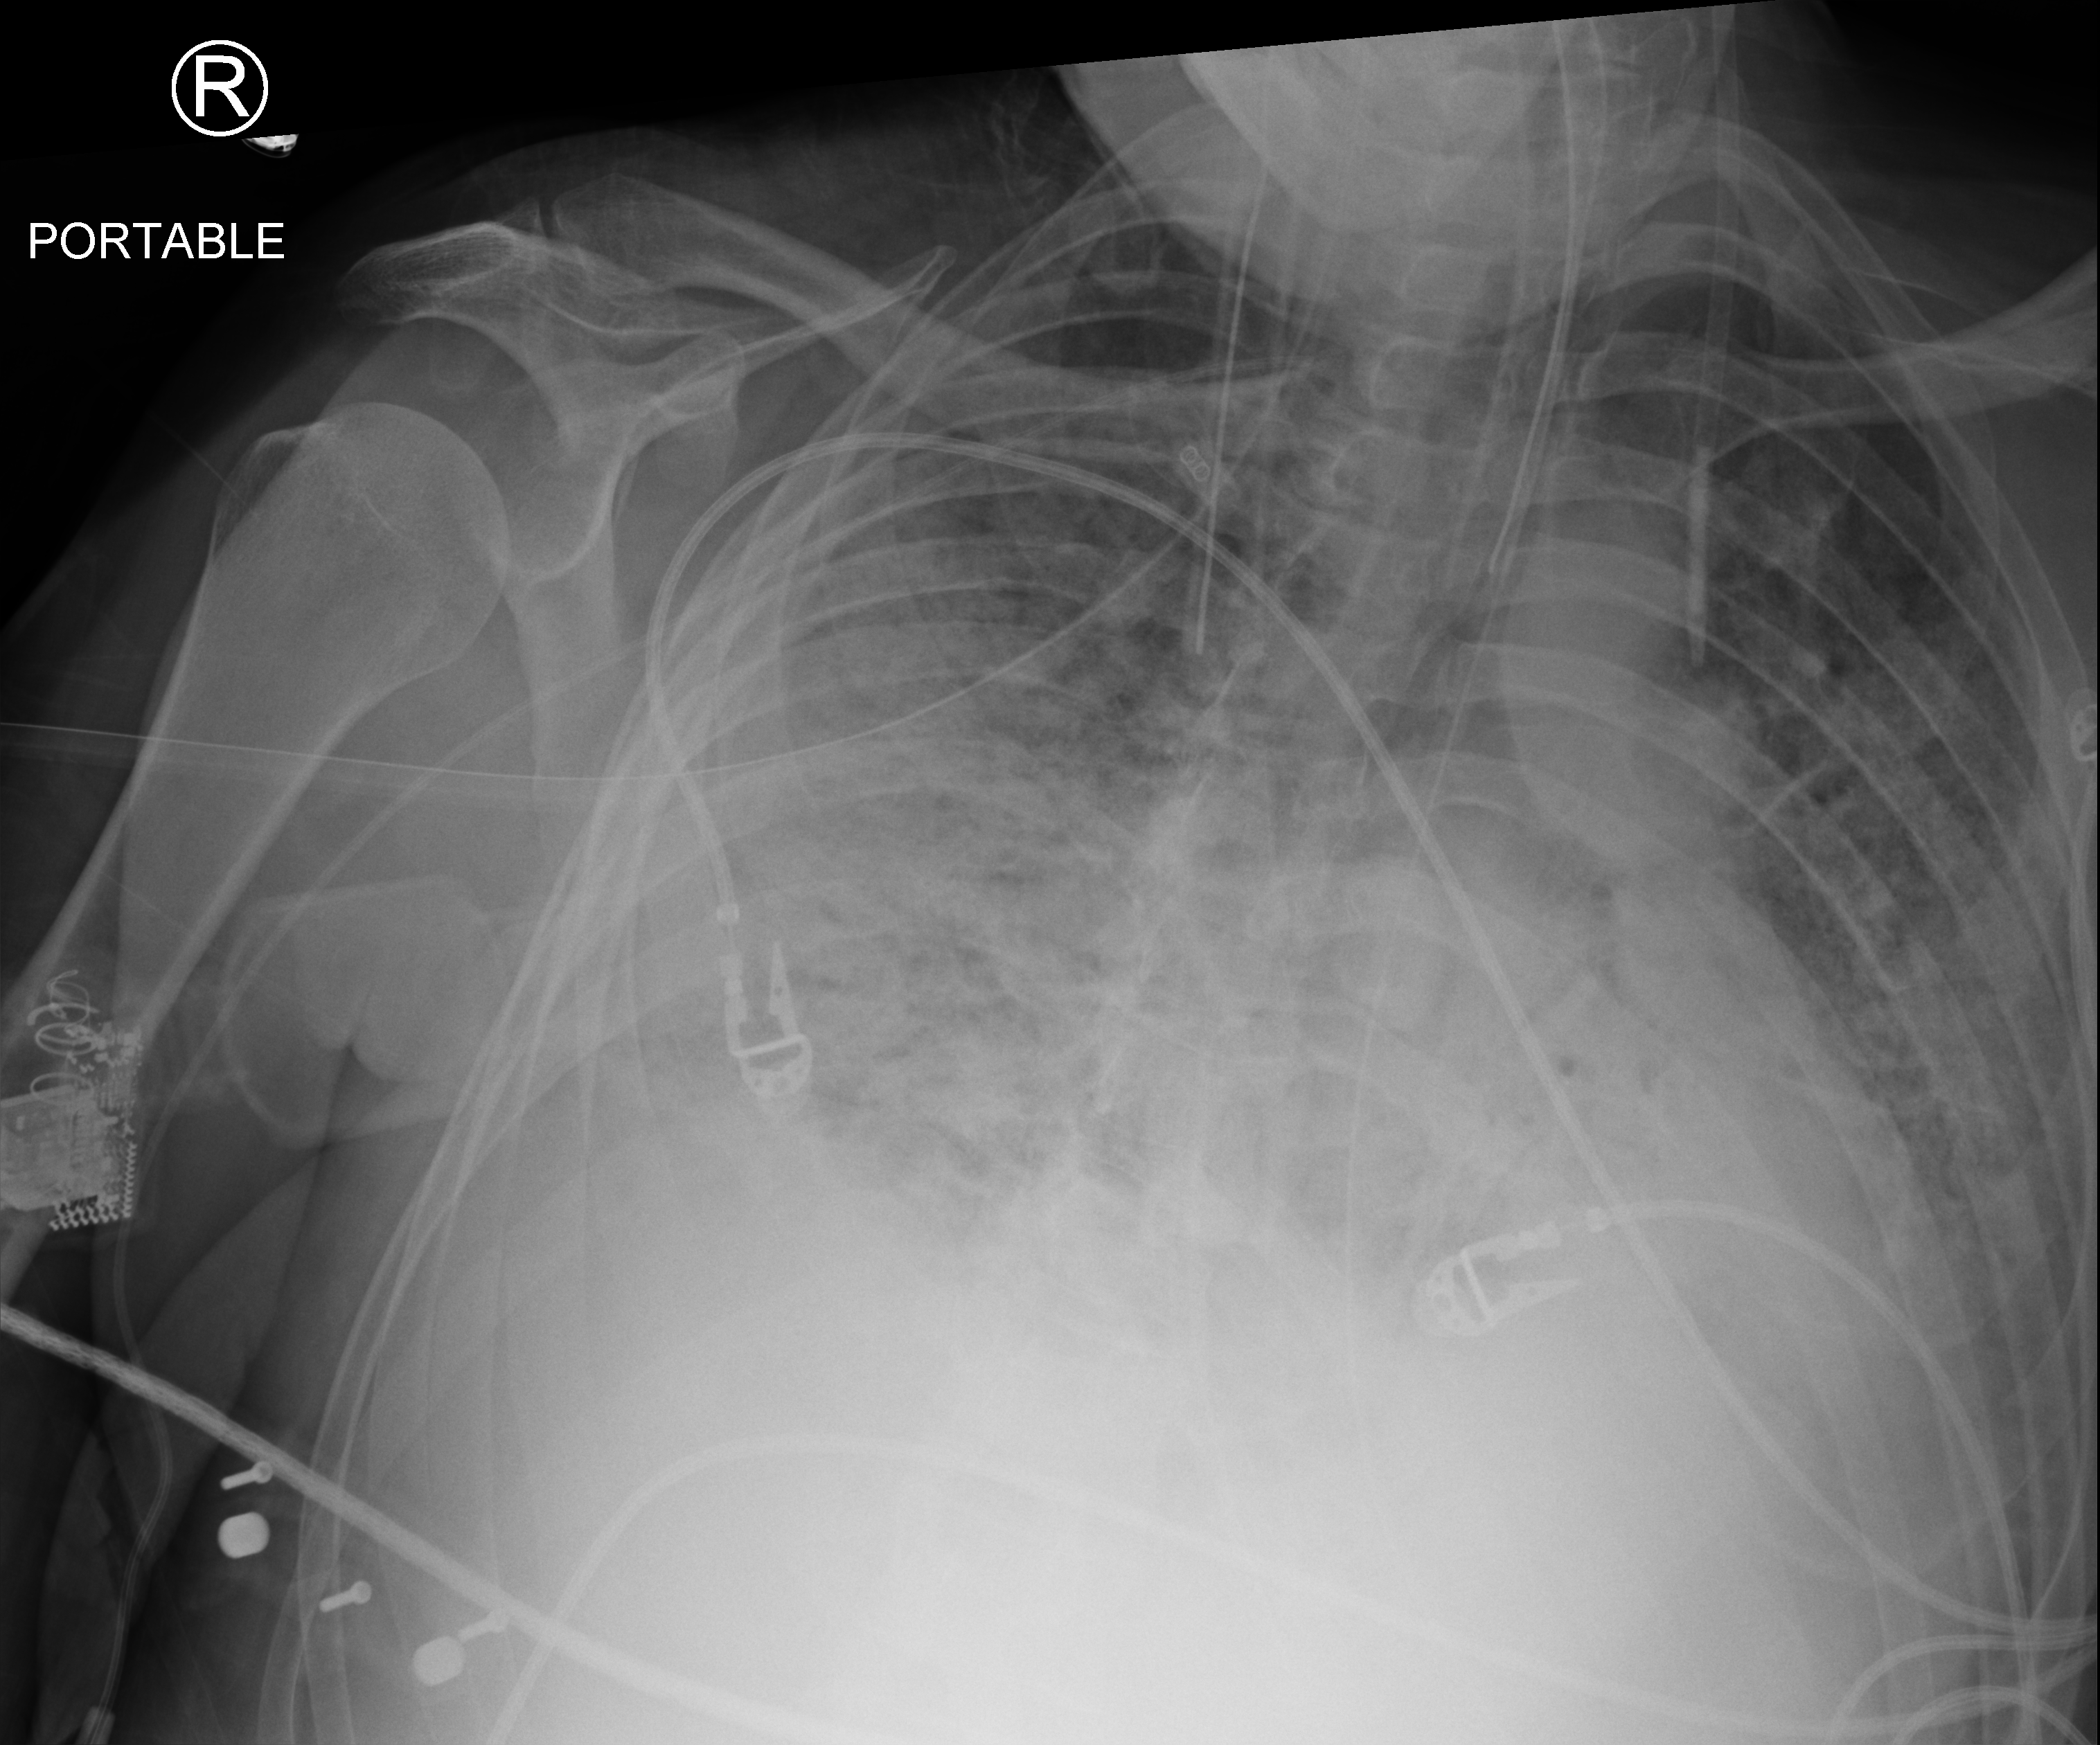
Portable chest radiograph, anteroposterior (AP) projection. Male patient hospitalised with COVID-19, age 18–59 years.
From the hospital-stay record, not from the radiograph (when in the stay this image was taken is not recorded): mechanically ventilated during this hospital stay: yes; diabetes (admission record): no; admitted to intensive care during this hospital stay: yes.